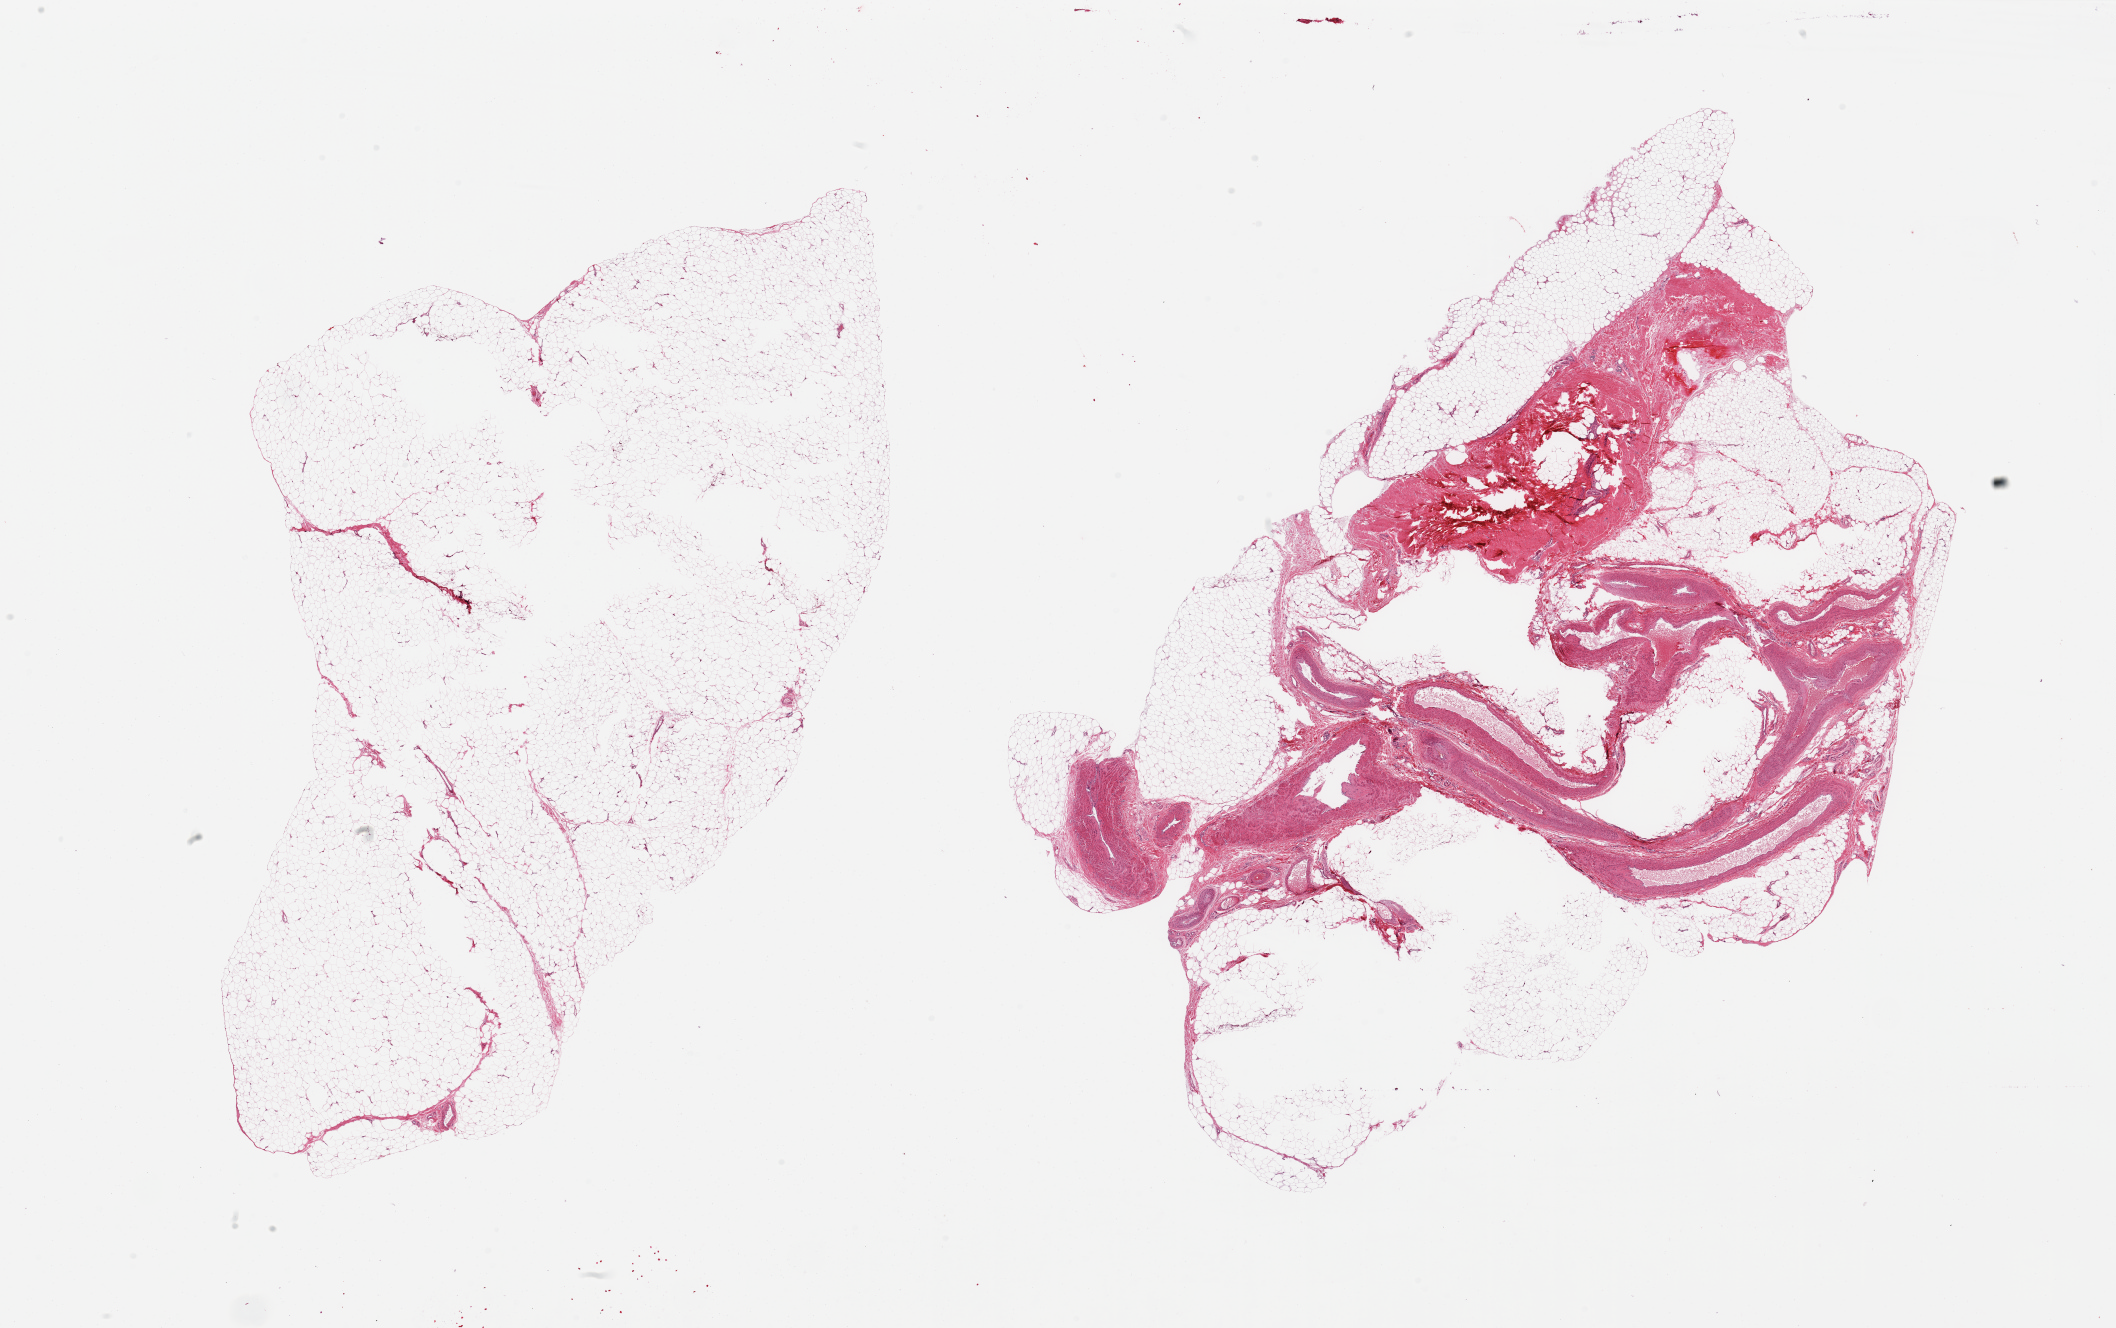
Whole-slide image, haematoxylin and eosin stain, brightfield — whole scanned area (about 33.5 x 21.0 mm, from a 20x scan) shown as a low-resolution overview. PAXgene-fixed, paraffin-embedded tissue. Section of adipose tissue (target tissue). Donor tissue sample. Donor sex: male.
- reviewer comment on this tissue sample: 2 pieces. 1 all fat, other with 50% vascular and fibrous content